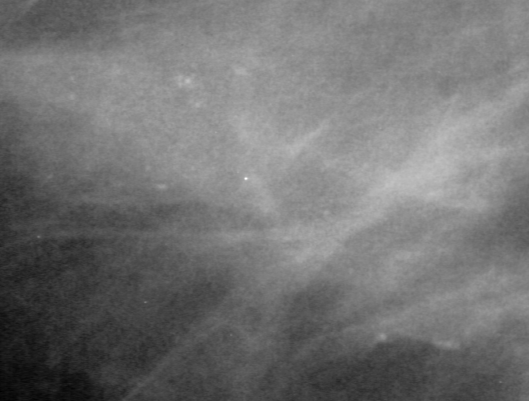
Crop from a digitized film mammogram around one marked abnormality; left breast; MLO view.
Marked abnormality: calcifications, morphology pleomorphic, distribution clustered; BI-RADS assessment category 4; pathology (as recorded): benign.